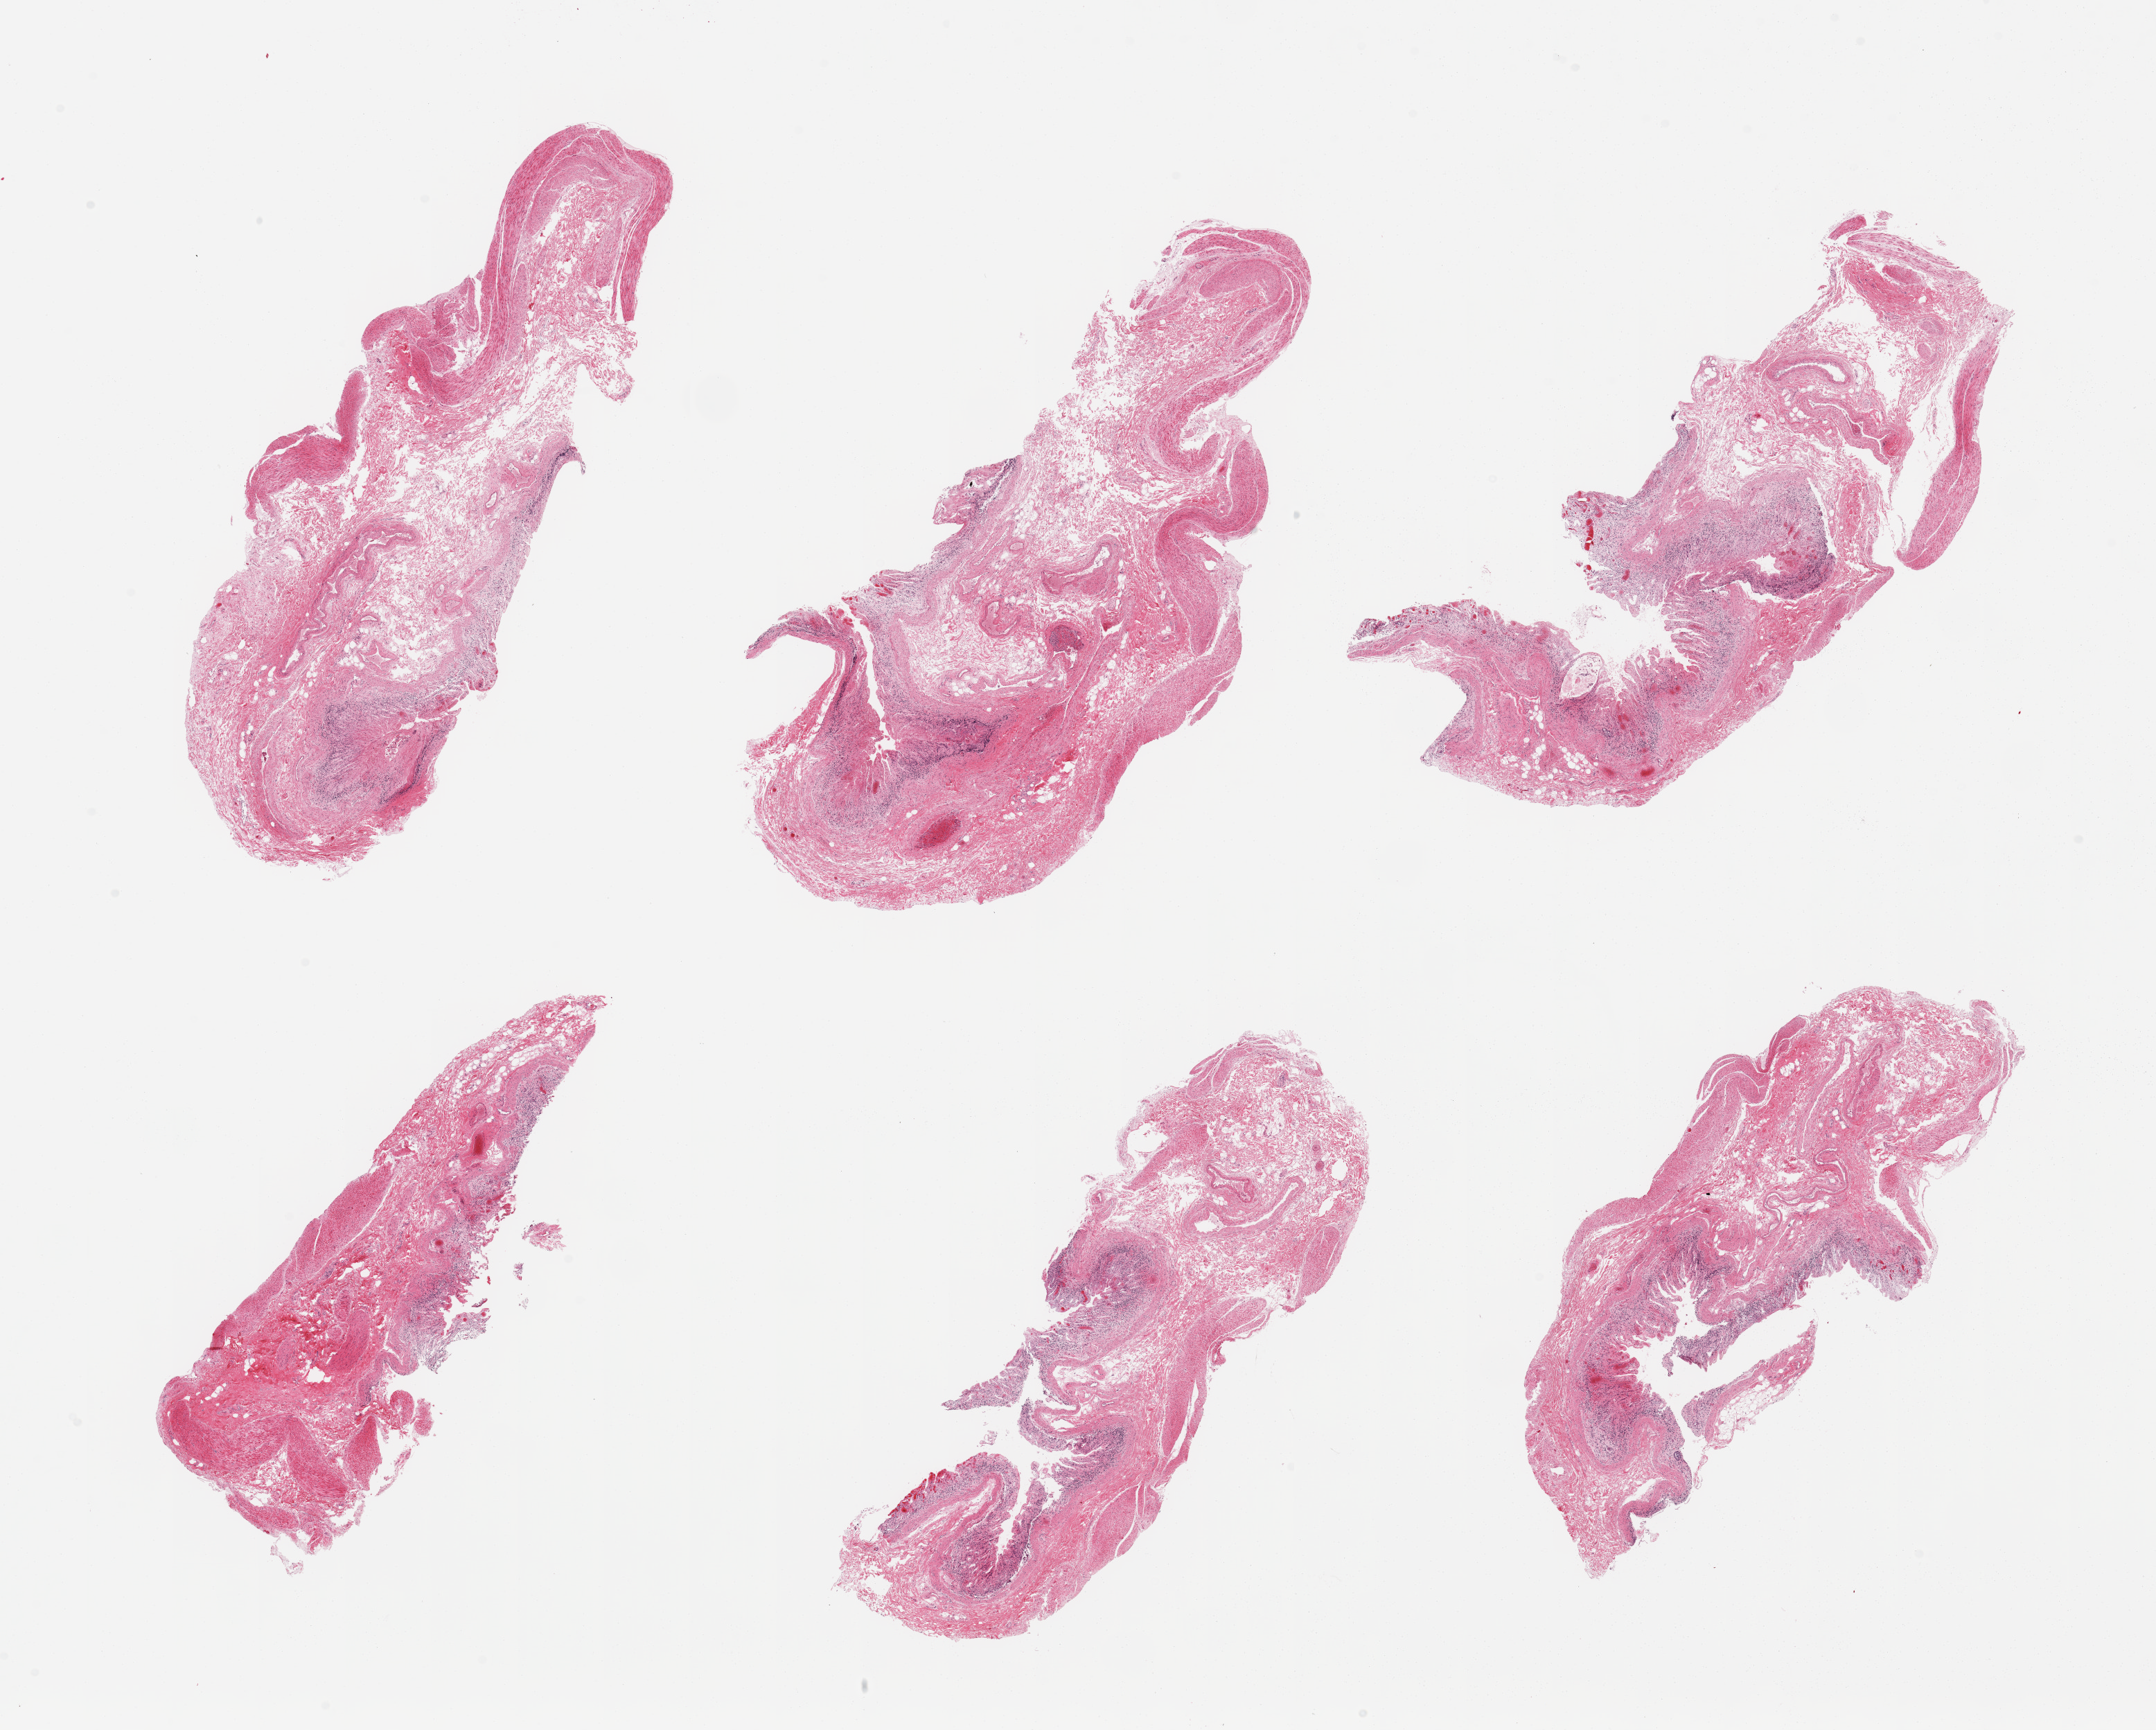
Hematoxylin and eosin (H&E) whole-slide image — whole scanned area (about 24.6 x 19.7 mm) shown as a low-resolution overview; PAXgene-fixed, paraffin-embedded tissue; sampled site (target tissue): stomach; tissue donor sample. Donor sex: male.
Review note (as recorded): 6 pieces, mucosa with markedly advanced autolysis.